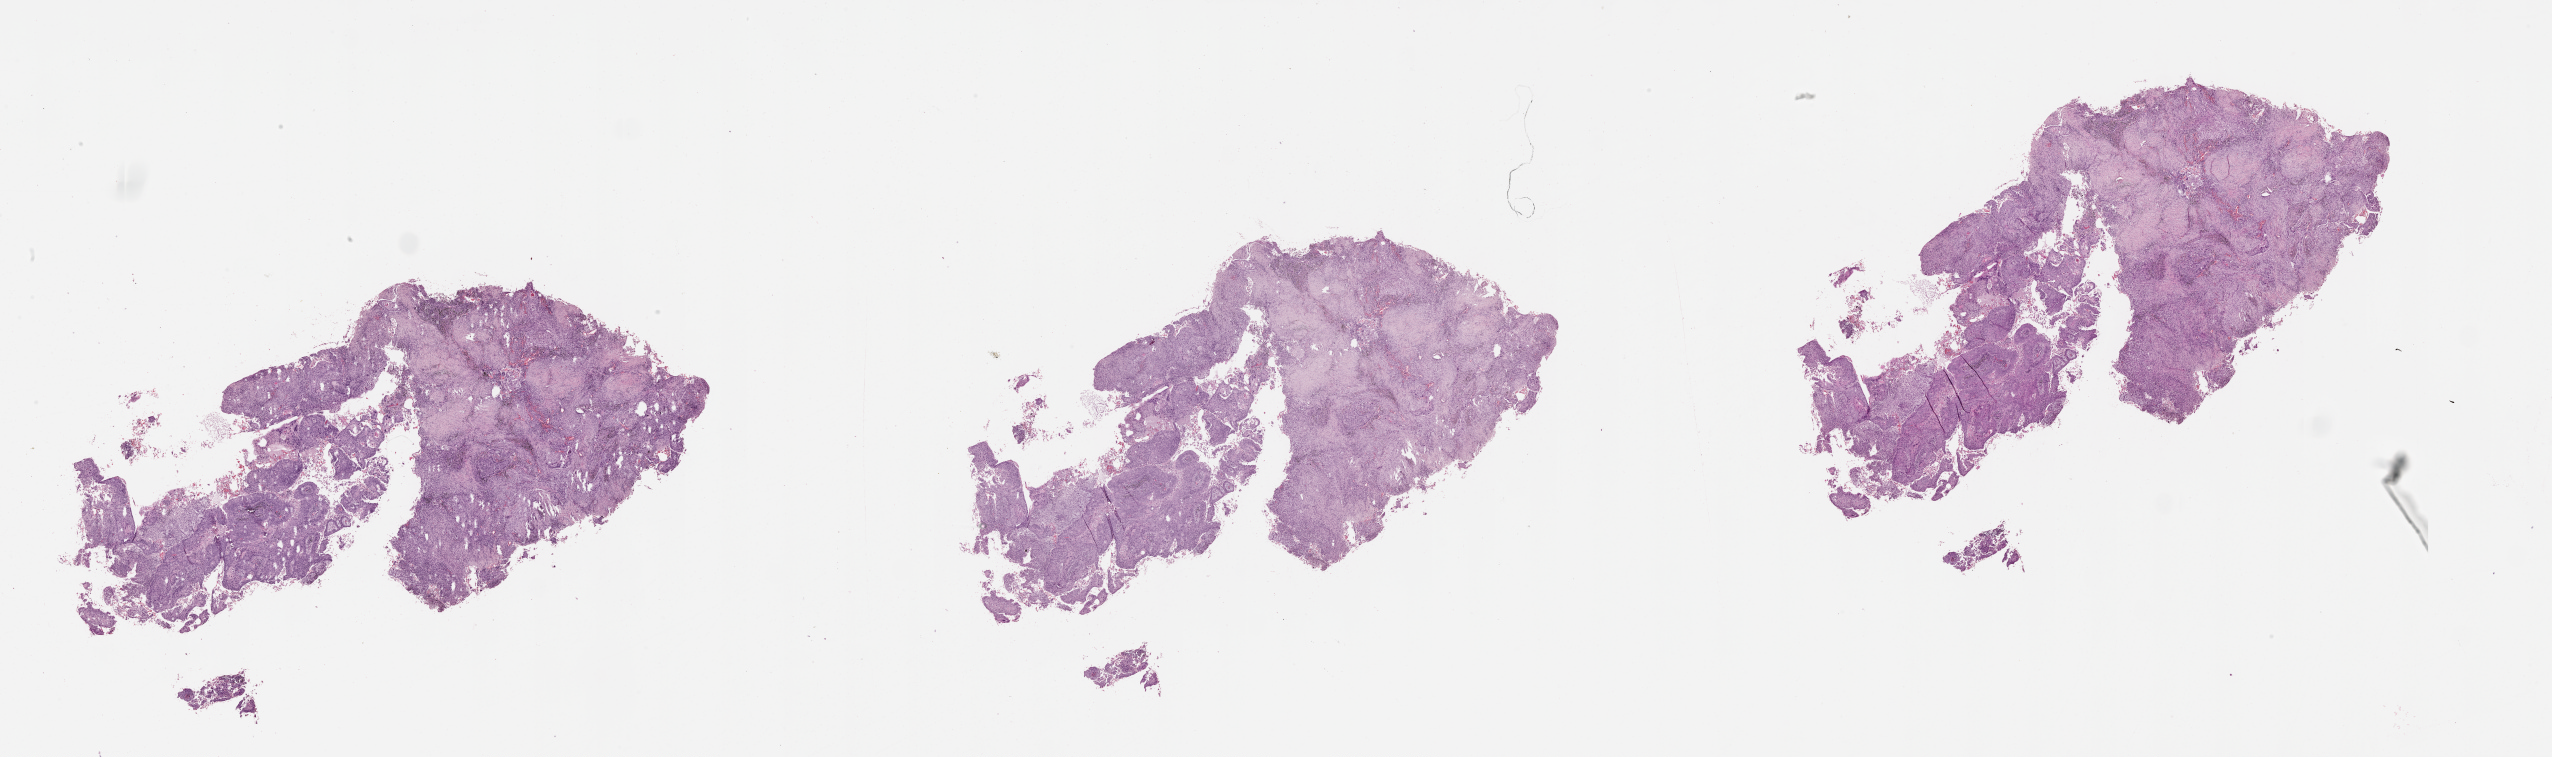
Whole-slide histology image, H&E-stained, whole scanned area (about 41.1 x 12.2 mm, slide scanned at 20x) shown as a low-resolution overview. Lung, tumour tissue. Male, 68 y/o.
- patient diagnosis (cohort enrolment): squamous cell carcinoma (lung)